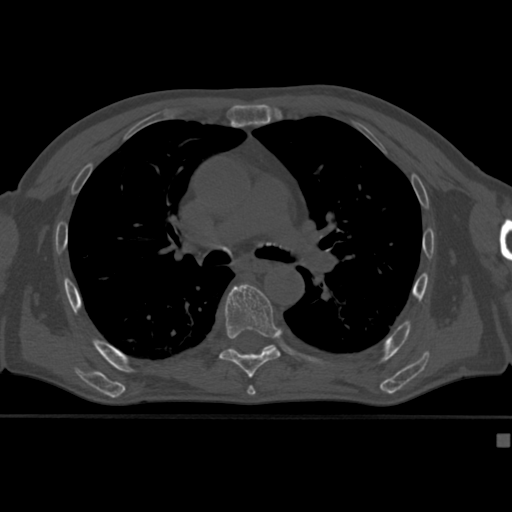
CT including the spine, one axial slice; position 279 of 430 along the scan axis; reconstruction kernel Br40s; 120 kVp; bone window (W 1800 / L 400 HU); 512 × 512 image matrix. Male patient, age 64 years. Case-level facts recorded for this patient, not image findings: primary cancer: uterus; vertebrae with lytic lesions (as recorded): T1, T4, T5, T7, L5.
Annotated regions visible in this slice (semi-automatically segmented with operator editing):
- T7 vertebra: bounding box <219,284,281,378> (left, top, right, bottom; pixels)